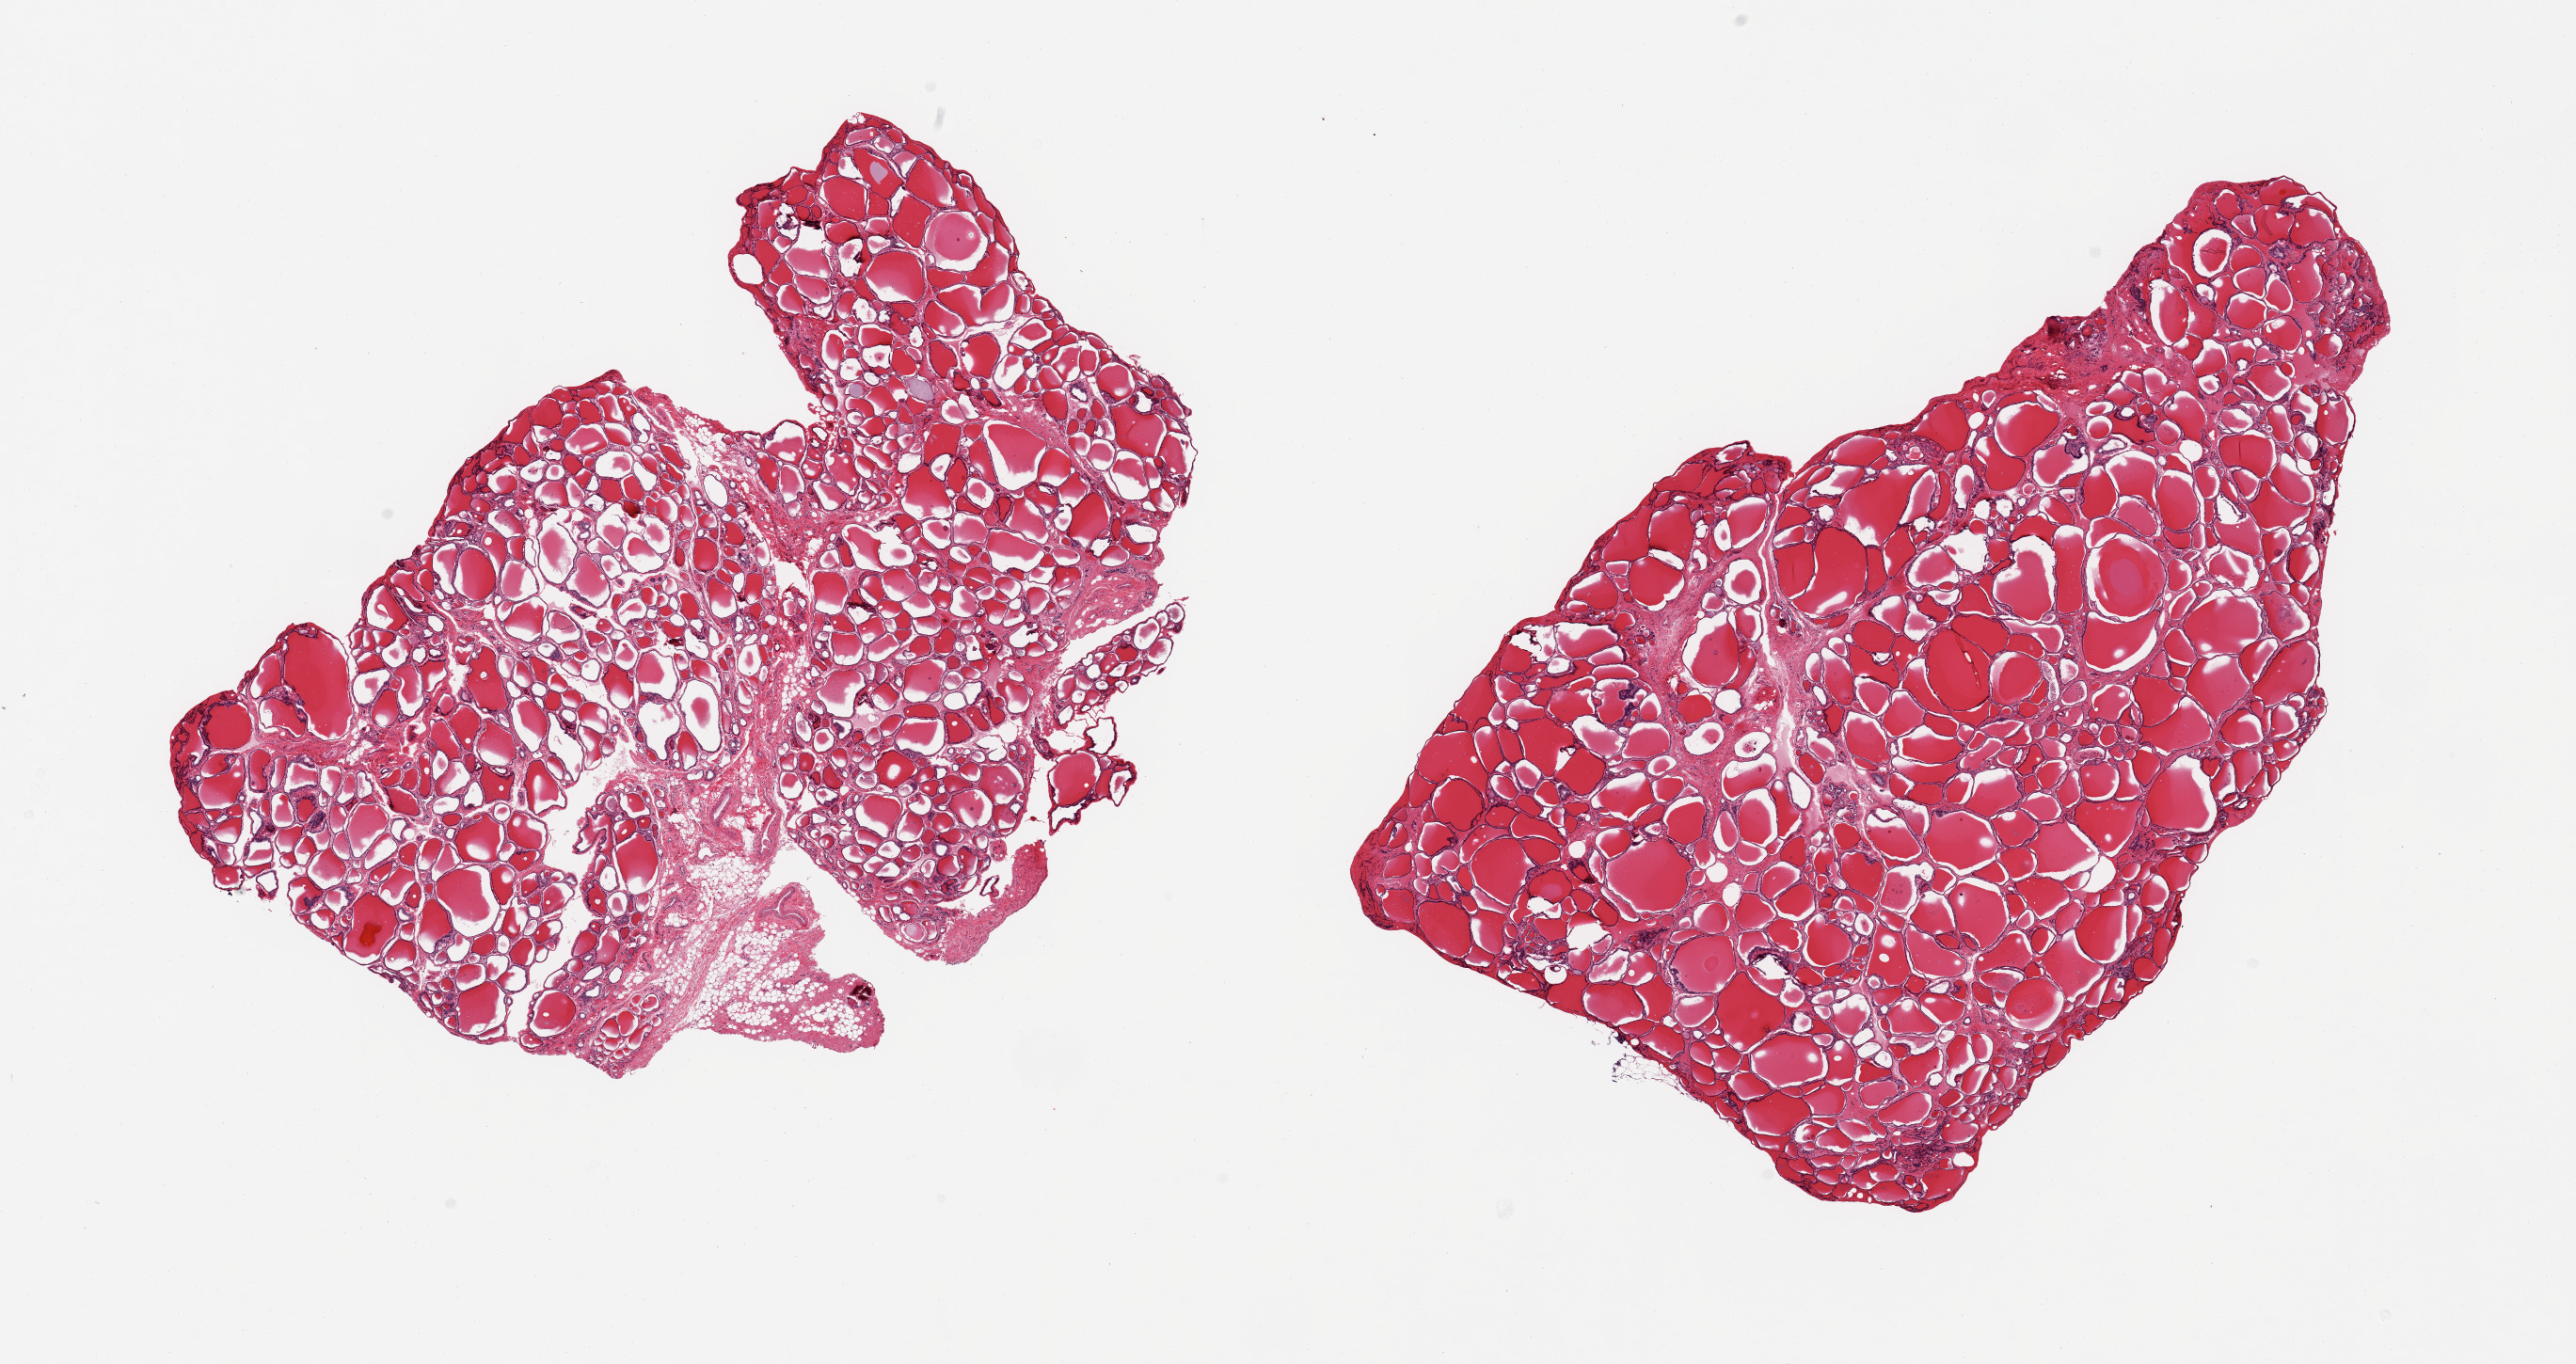
H&E whole-slide image, brightfield — low-resolution overview of the scanned area, about 21.7 x 11.5 mm, PAXgene-fixed, paraffin-embedded tissue, target tissue: thyroid, tissue donor sample. Donor sex: female.
Review note (as recorded): 2 pieces, no abnormalities.